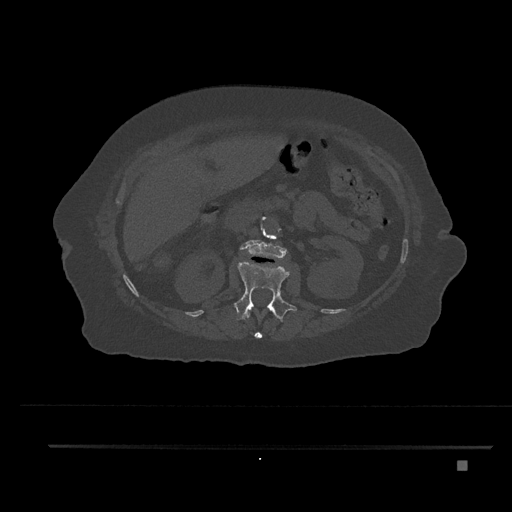
CT including the spine, one axial slice. Position 220 of 797 along the scan axis. Reconstruction kernel Br40s/3. Bone window (W 1800 / L 400 HU). 512 × 512 image matrix, field of view 437 × 437 mm. Female patient, age 76 years. Case-level facts recorded for this patient, not image findings: primary cancer: lung; vertebrae with lytic lesions (as recorded): T11, L3.
Annotated regions visible in this slice (semi-automatic segmentation, software-assisted and operator-edited):
- L1 vertebra: bounding box <235,261,297,322> (left, top, right, bottom; pixels)
- L2 vertebra: <240,240,287,259>
- T12 vertebra: <245,311,276,339>